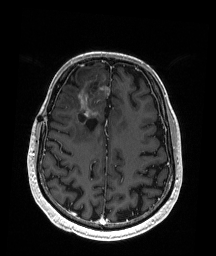
Brain MRI from a brain-tumour surgery series, one axial slice; slice 65 of 192 in the series (ordered by position); T1-weighted post-contrast; 1 mm slice thickness; 216 × 256 image matrix. Case-level facts recorded for this patient, not image findings: histopathology: Astrocytoma; WHO grade: 3; IDH mutation: yes.
Structures marked on this image (manually delineated by an expert):
- previous resection cavity: bounding box <79,81,99,122> (left, top, right, bottom; pixels)
- tumour: <79,81,109,117>